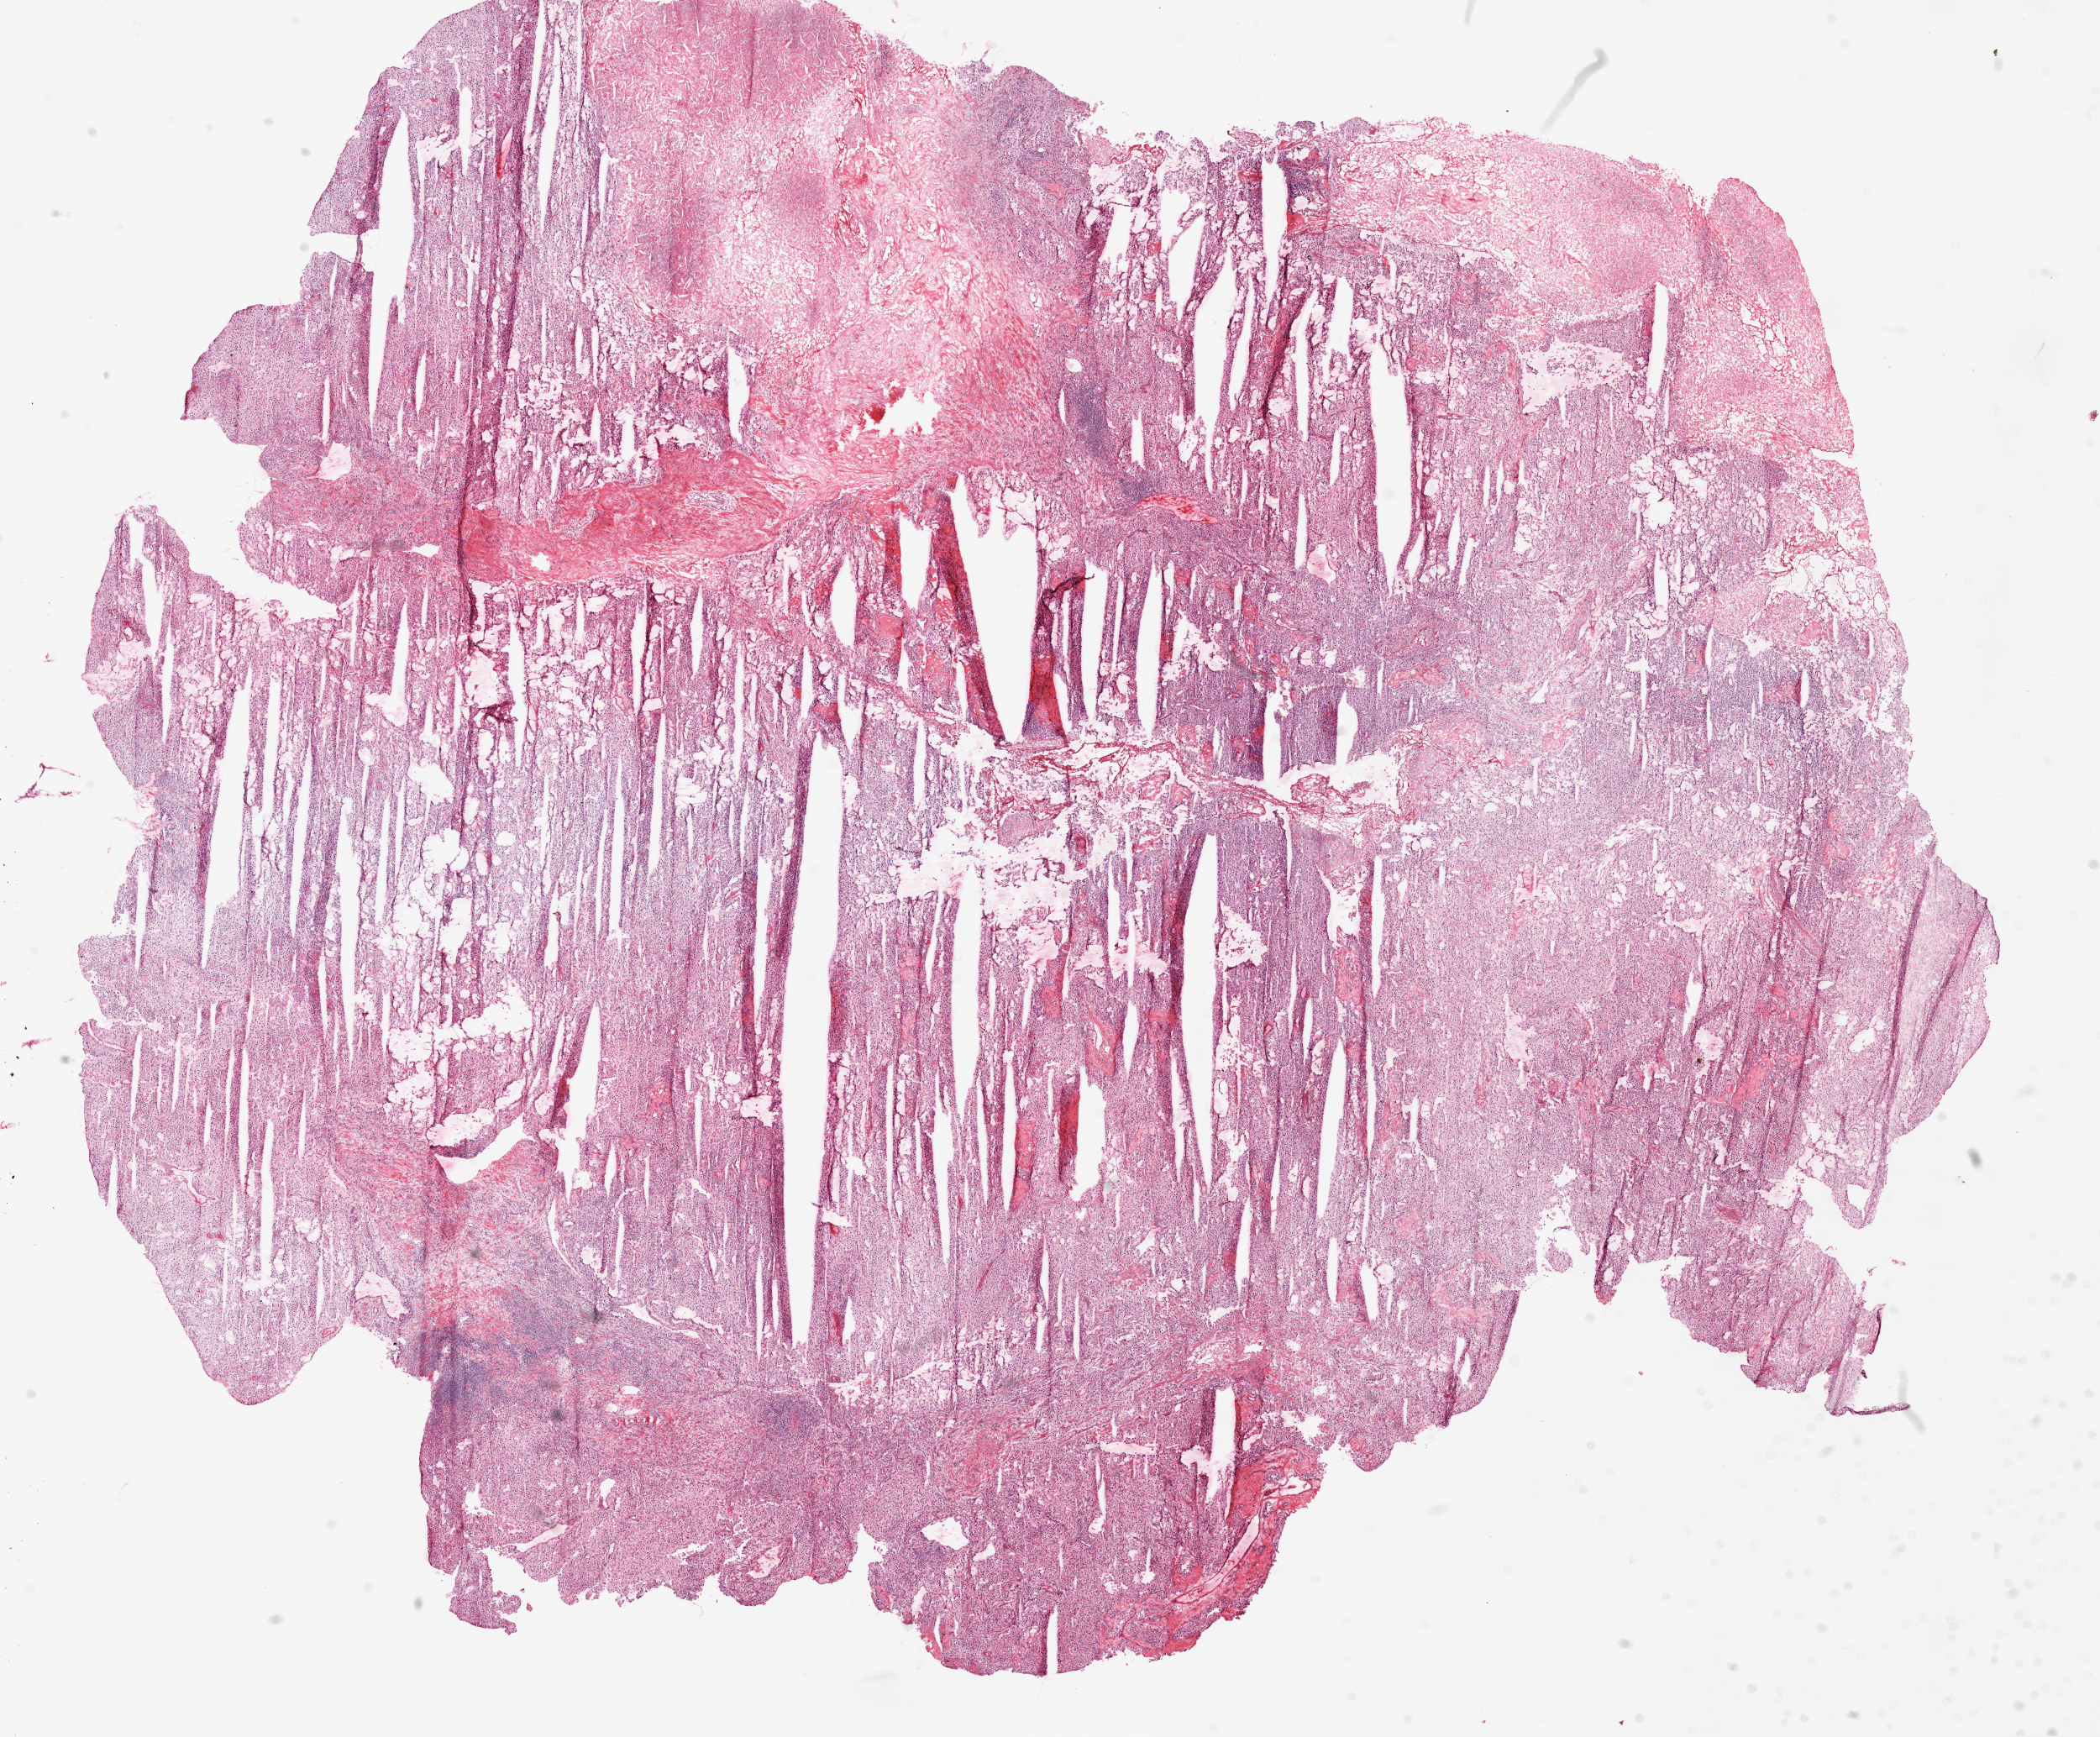
Whole-slide histology image, H&E — a low-resolution overview of the entire scanned area, about 20.1 x 16.6 mm (from a 20x scan); frozen section; sample: primary tumour, kidney. Male patient; age at initial diagnosis 41 years. Histologic grade: G2 (moderately differentiated). Composition of this section per pathologist review: tumour cells 75%, tumour nuclei 80%, normal cells 0%, stromal cells 10%, necrosis 15%. Infiltration values recorded for this section: lymphocyte infiltration 5%, monocyte infiltration 0%, neutrophil infiltration 0%.
Histologic diagnosis: Clear cell adenocarcinoma, NOS. Laterality: left. TNM: T2 N0 M0. AJCC pathologic stage: II (6th edition).